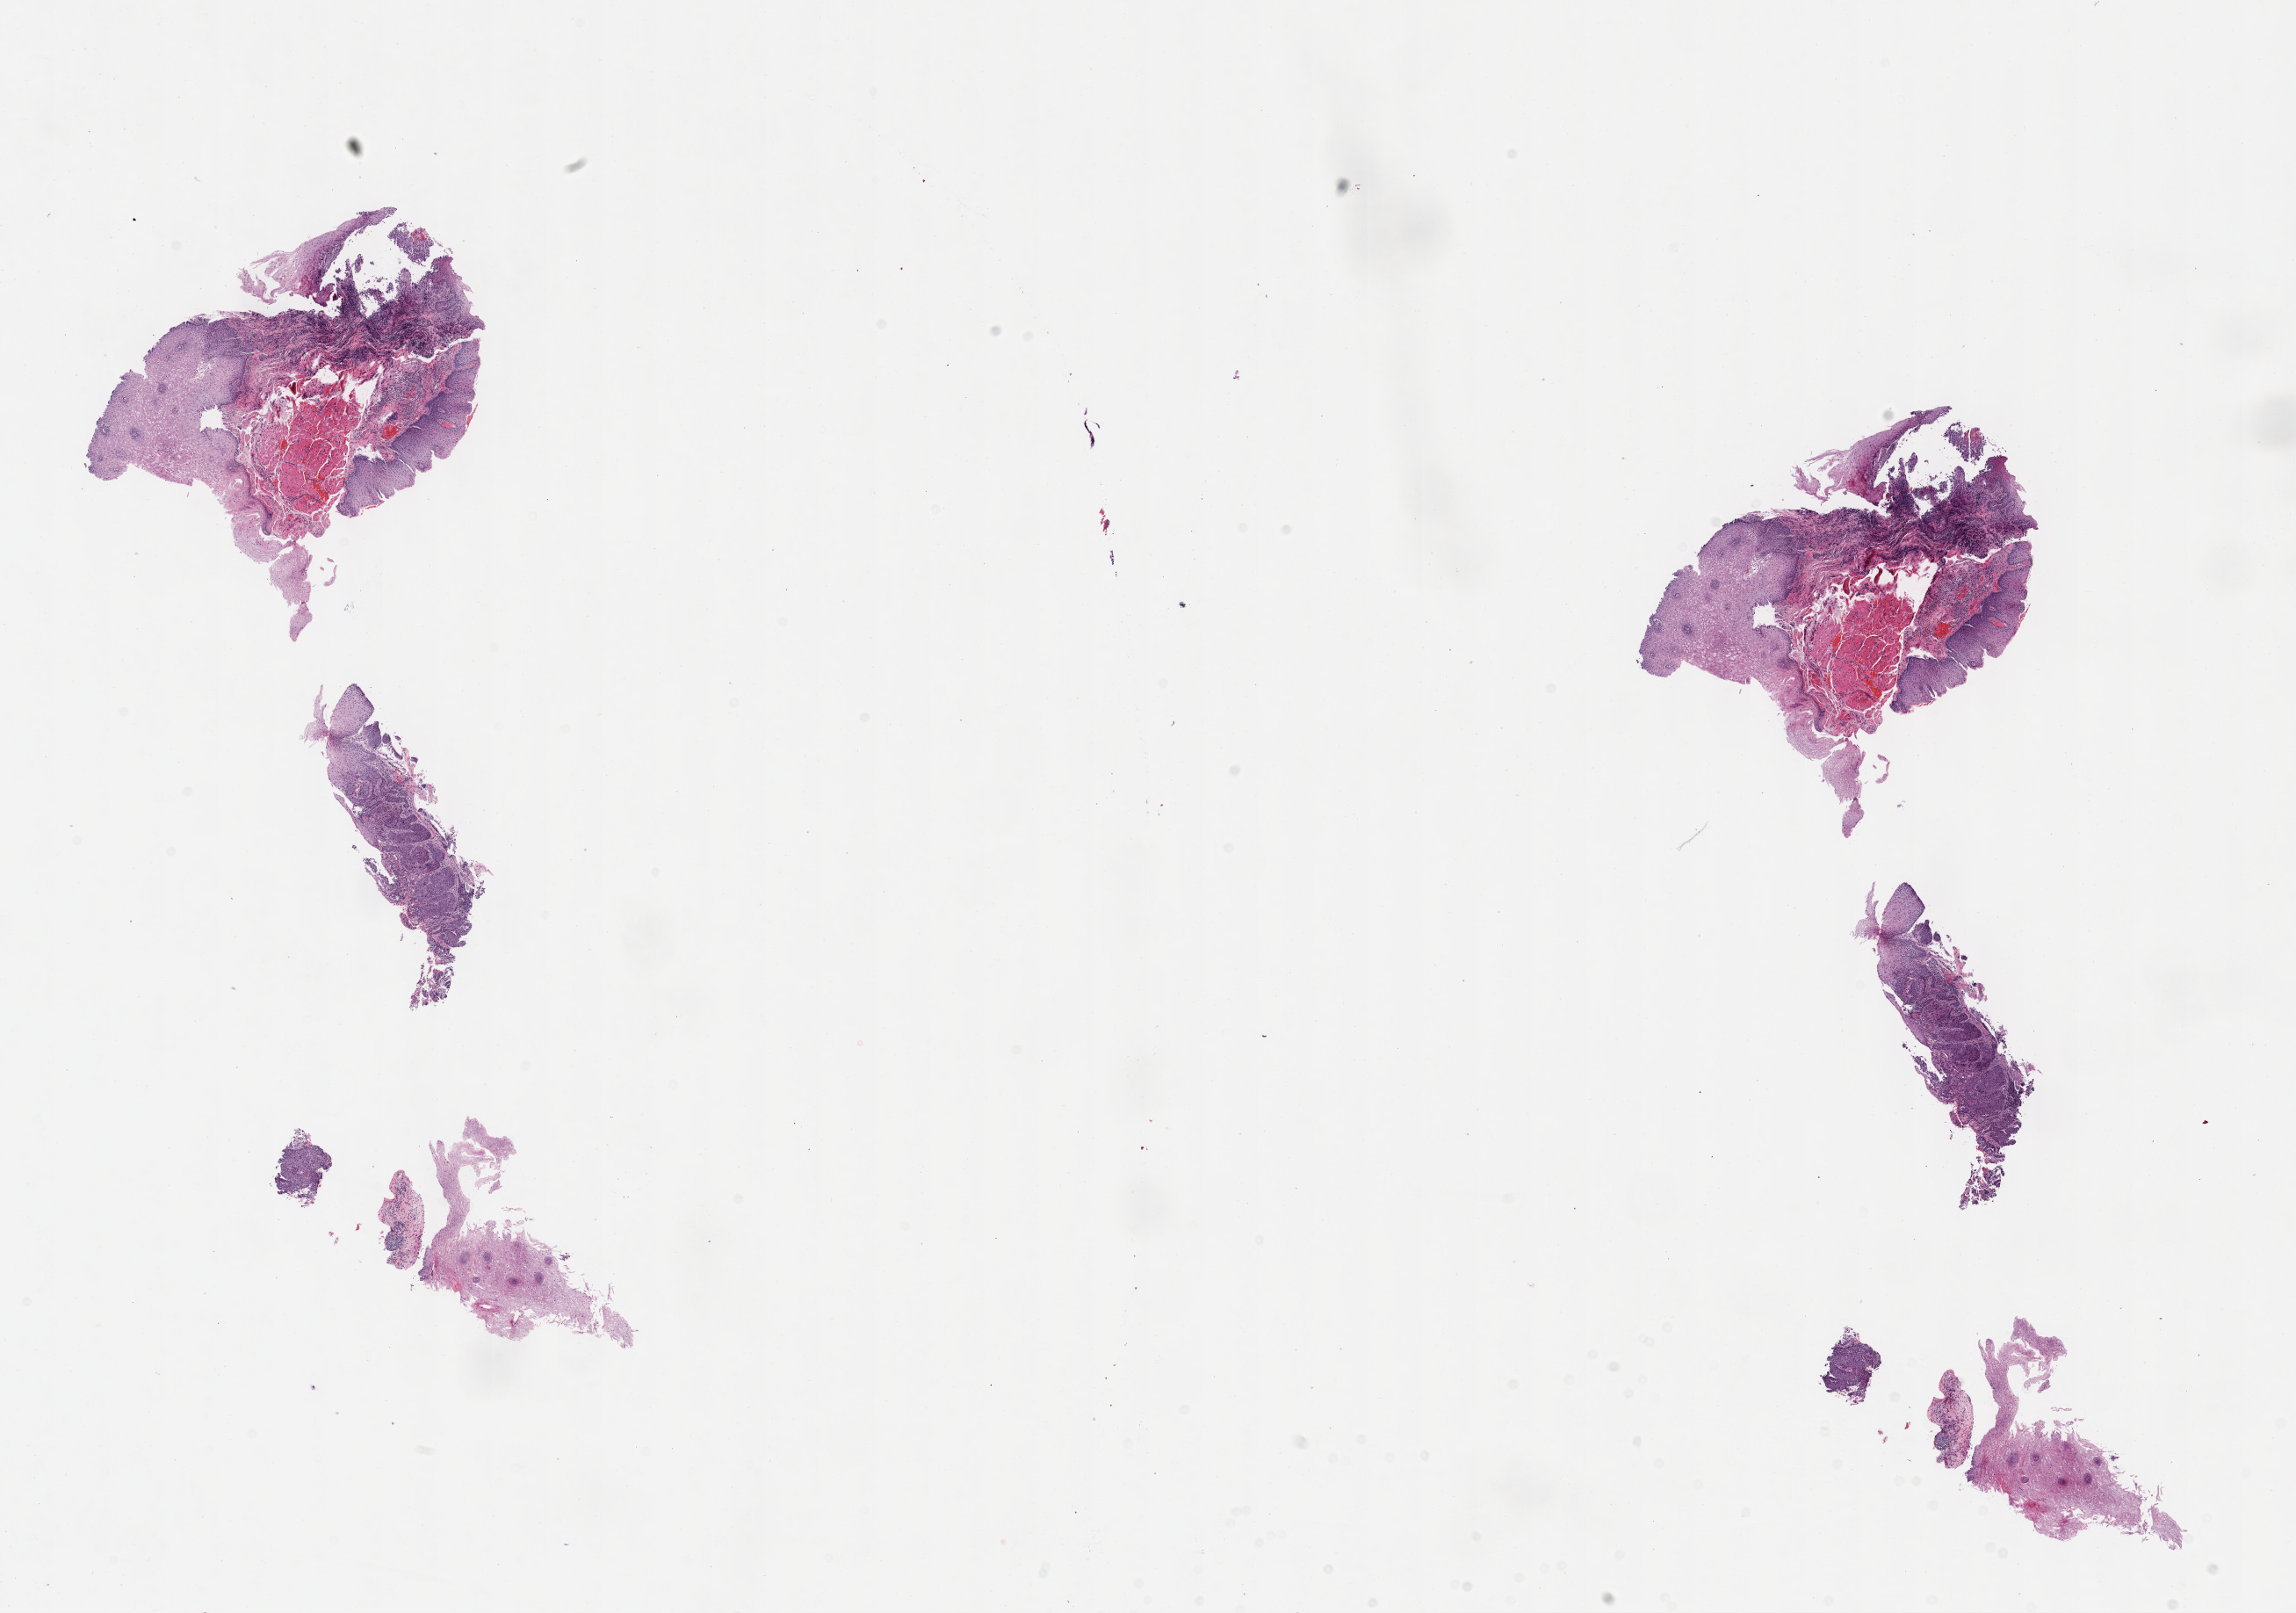
Whole-slide histology image, H&E, whole scanned area (about 21.1 x 14.8 mm, acquisition: 40x scan) shown as a low-resolution overview, FFPE section, sample: primary tumour, esophagus. Male, age 82 years at initial diagnosis. Histologic grade: GX (grade cannot be assessed).
AJCC pathologic stage: IA (7th edition). Diagnosis: Squamous cell carcinoma, NOS. TNM: T1 N0 M0.